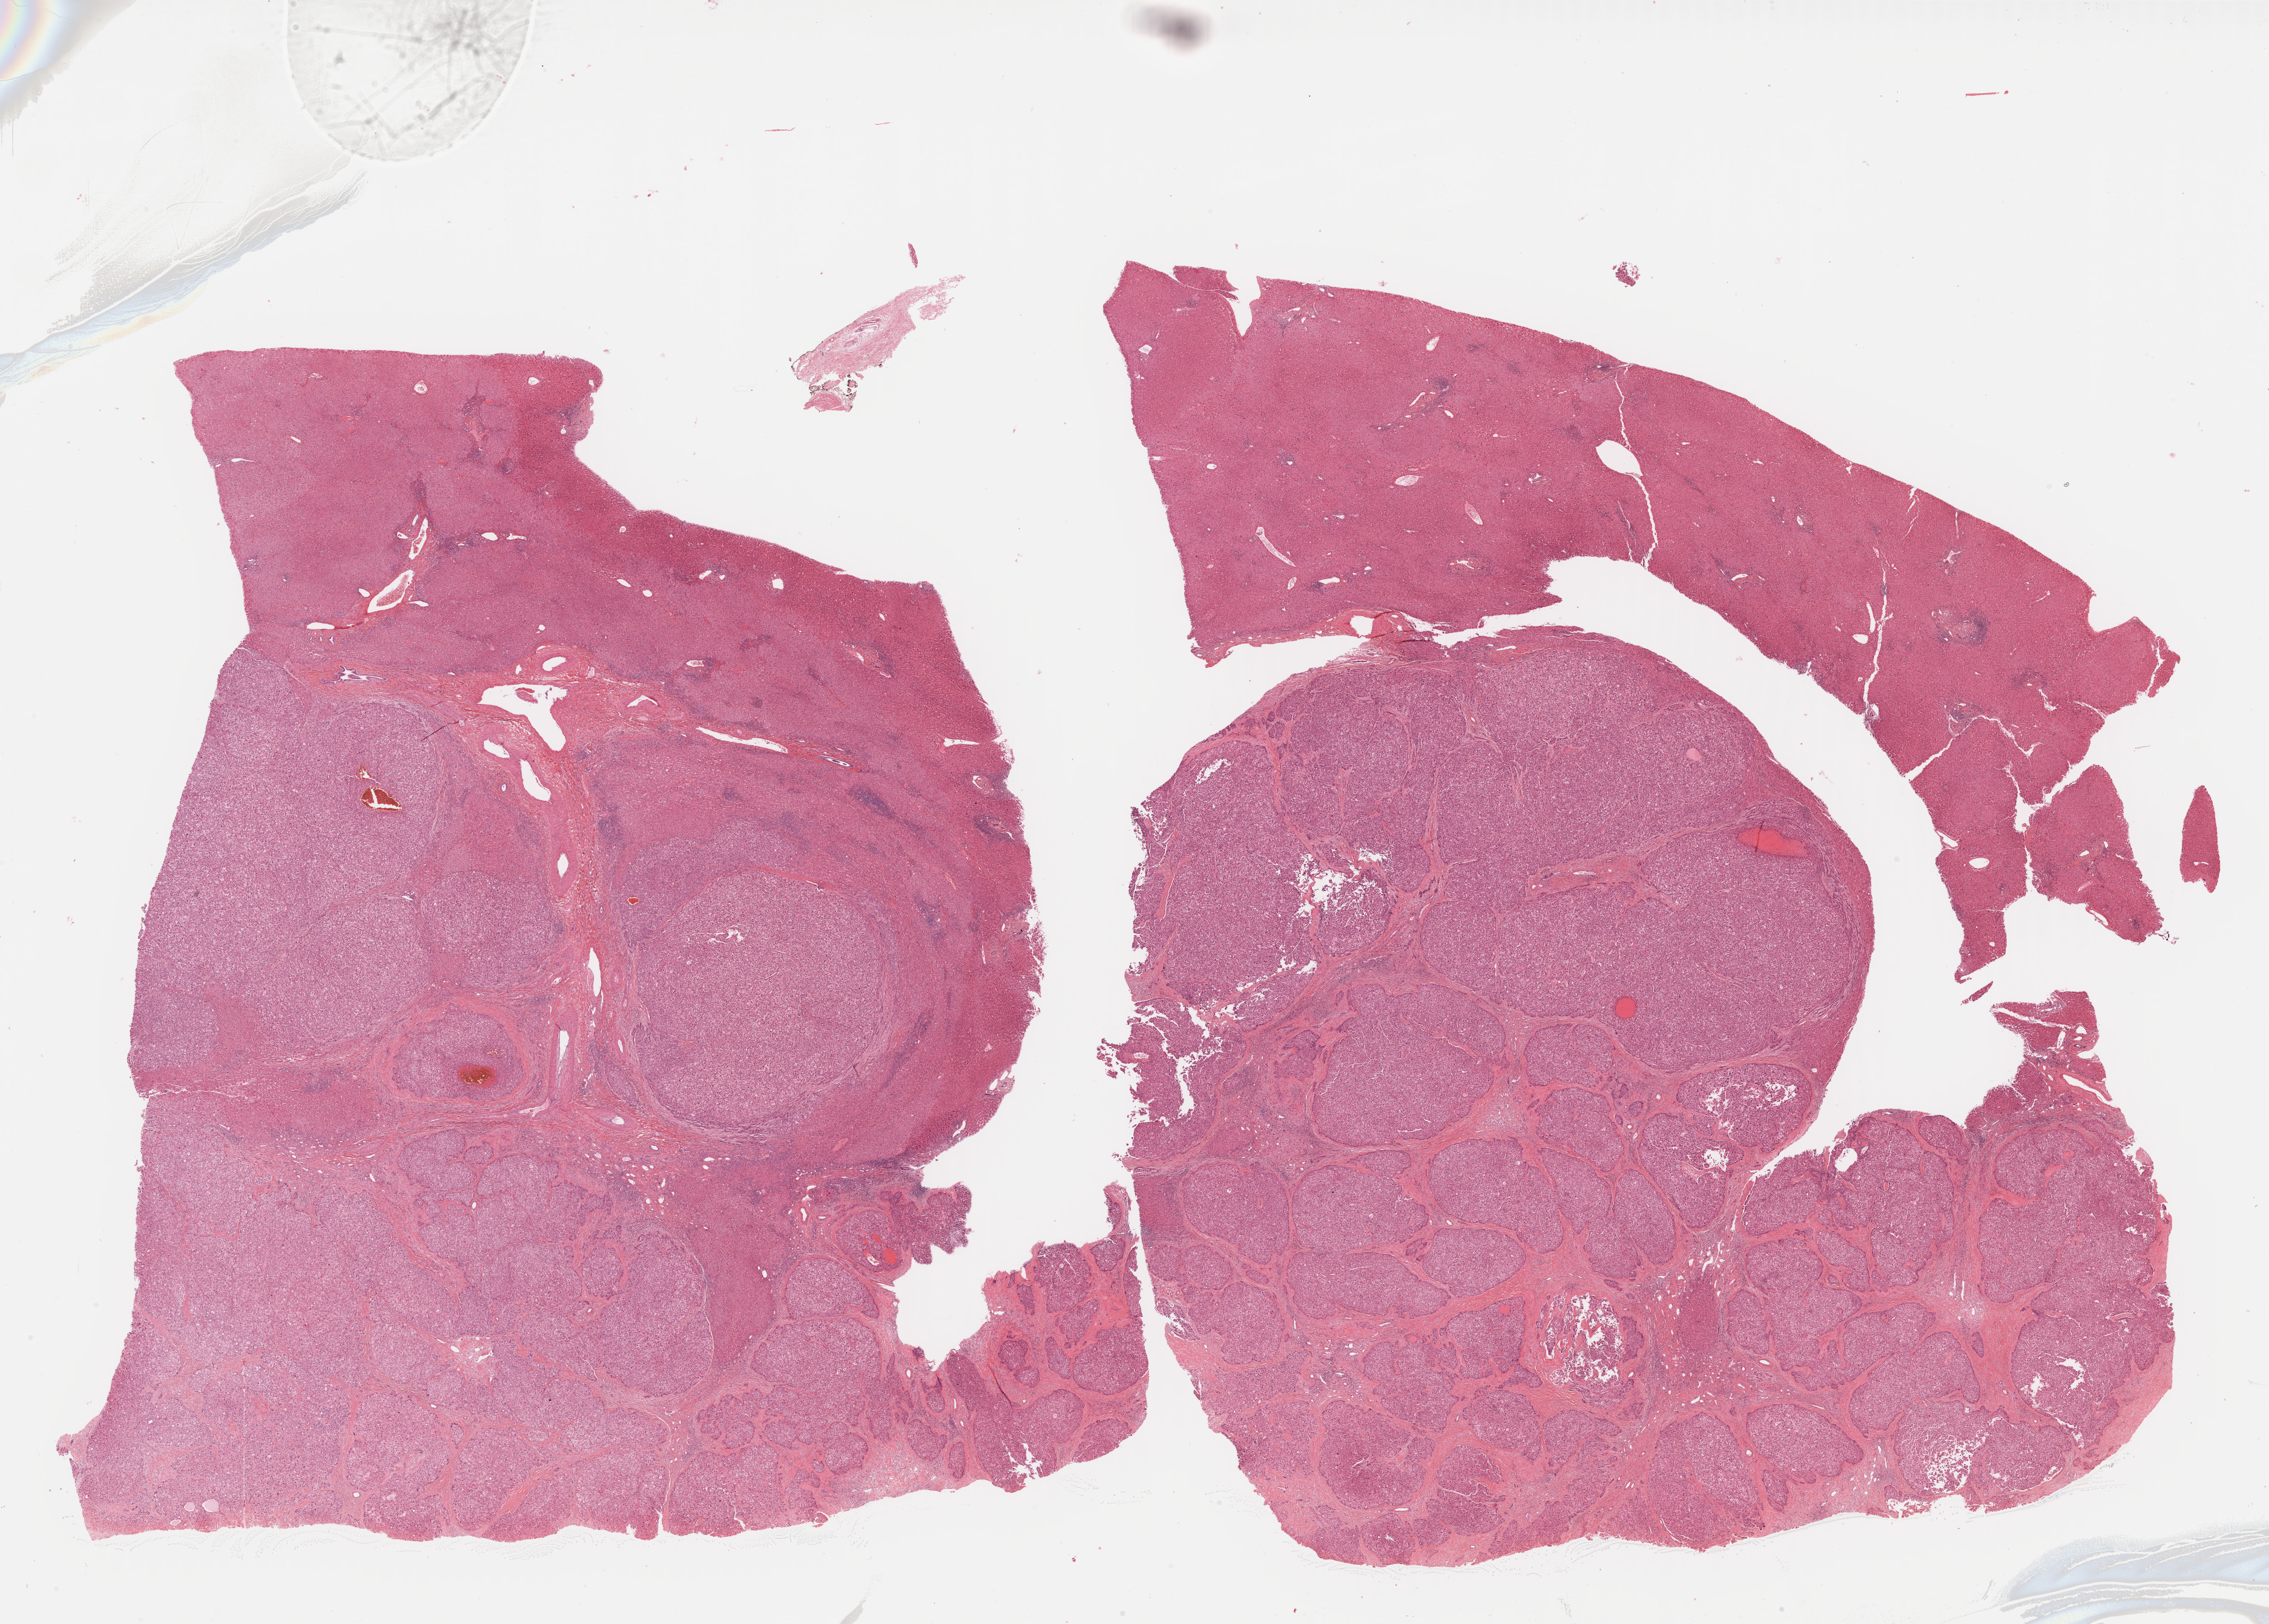
Digitized H&E-stained tissue section (whole slide), shown as a low-resolution overview of the whole scanned area (about 30.3 x 21.7 mm), formalin-fixed paraffin-embedded (FFPE) diagnostic section, primary tumour sample from the liver. Male, age 70 years at initial diagnosis. Histologic grade: G2 (moderately differentiated).
TNM: T1 NX M0. Diagnosis: Hepatocellular carcinoma, NOS. AJCC pathologic stage: I (5th edition).